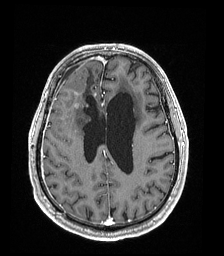
Brain MRI from a brain-tumour surgery series, one axial slice. Position 68 of 192 along the scan axis. T1-weighted post-contrast. 1 mm slice thickness. 224 × 256 image matrix, field of view 224 × 256 mm. Case-level facts recorded for this patient, not image findings: histopathology: Astrocytoma; WHO grade: 4; IDH mutation: yes.
Structures marked on this image (outlined manually by an expert reader):
- previous resection cavity: bounding box <84,108,88,114> (left, top, right, bottom; pixels)